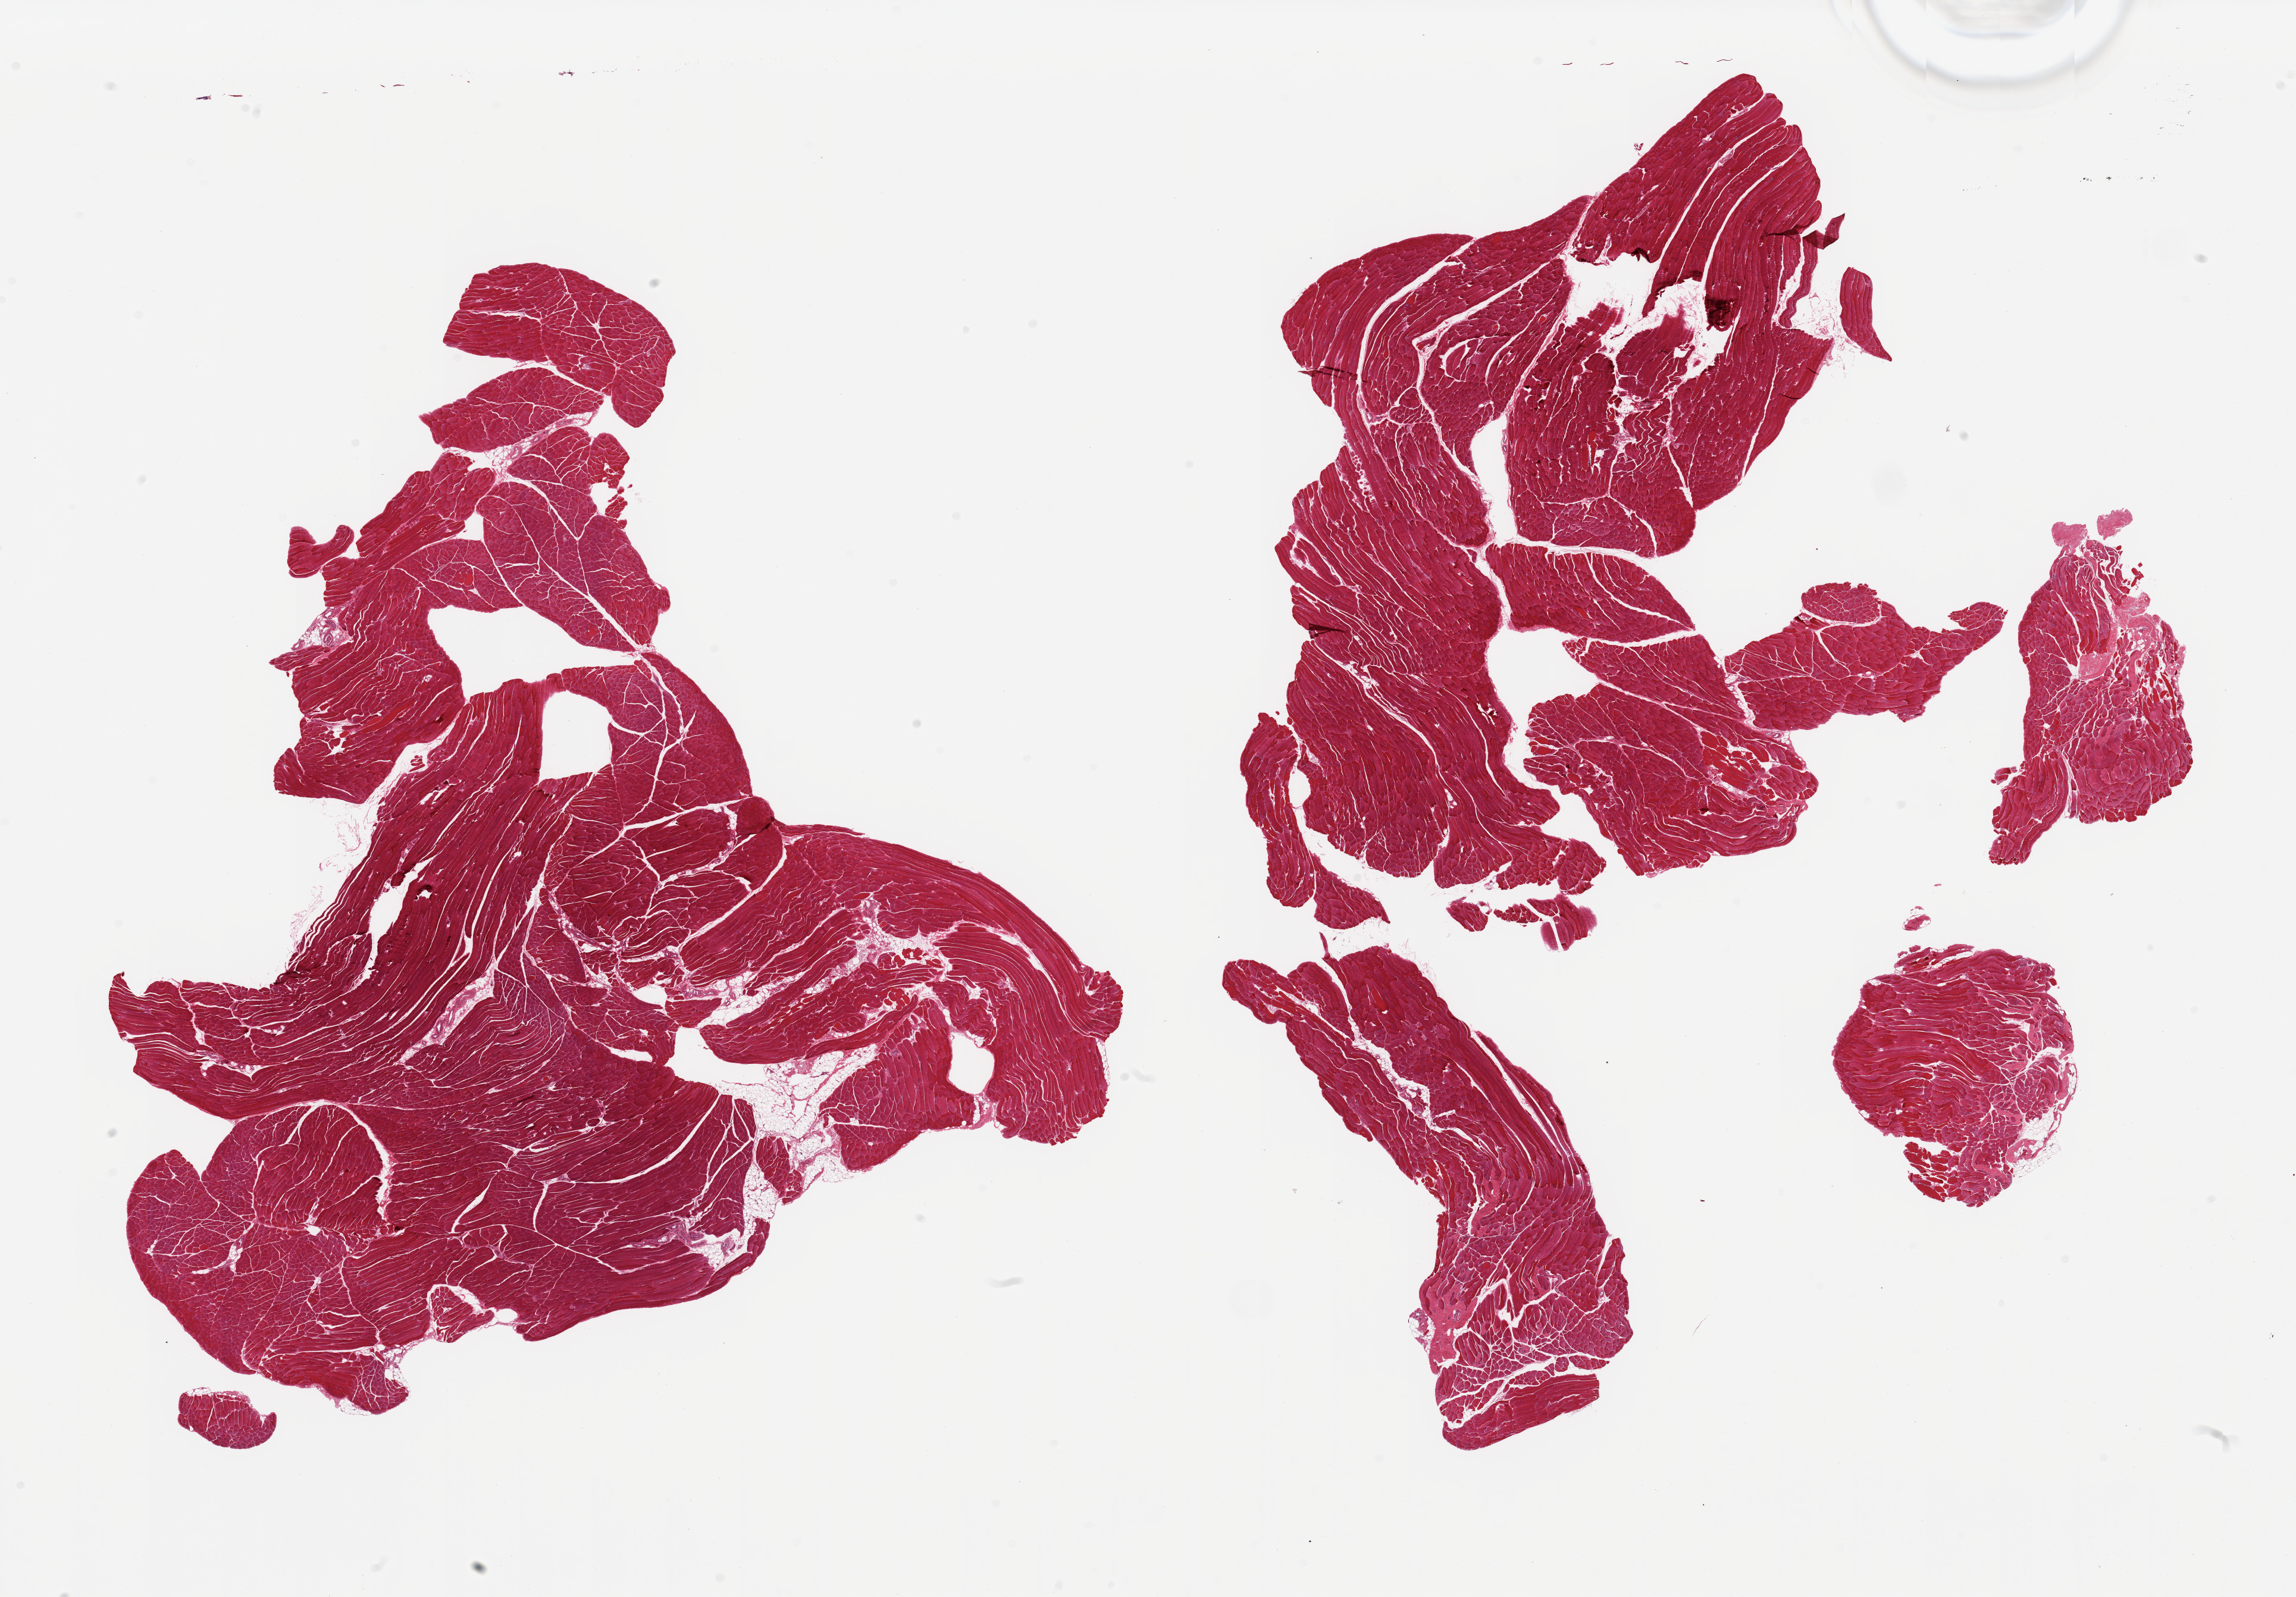
H&E whole-slide image — a low-resolution overview of the entire scanned area, about 30.5 x 21.2 mm (from a 20x scan). PAXgene-fixed, paraffin-embedded tissue. Section of skeletal muscle (target tissue). Tissue donor sample.
Review note (as recorded): 2 pieces, minimal interstitial fat.